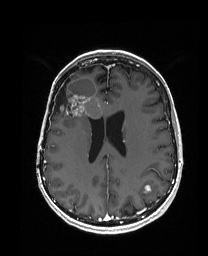
Brain MRI from a brain-tumour surgery series, one axial slice. Slice 72 of 192 in the series (ordered by position). T1-weighted post-contrast. 1 mm slice thickness. 208 × 256 image matrix, field of view 203 × 250 mm. From the clinical record (not read from this slice): histopathology: Metastatic Carcinoma from Breast primary; tumour location: Right Frontal.
Annotated regions visible in this slice (manually delineated by an expert):
- previous resection cavity: bounding box (x1, y1, x2, y2) in pixels: (53, 78, 70, 113)
- tumour: (55, 77, 104, 128)